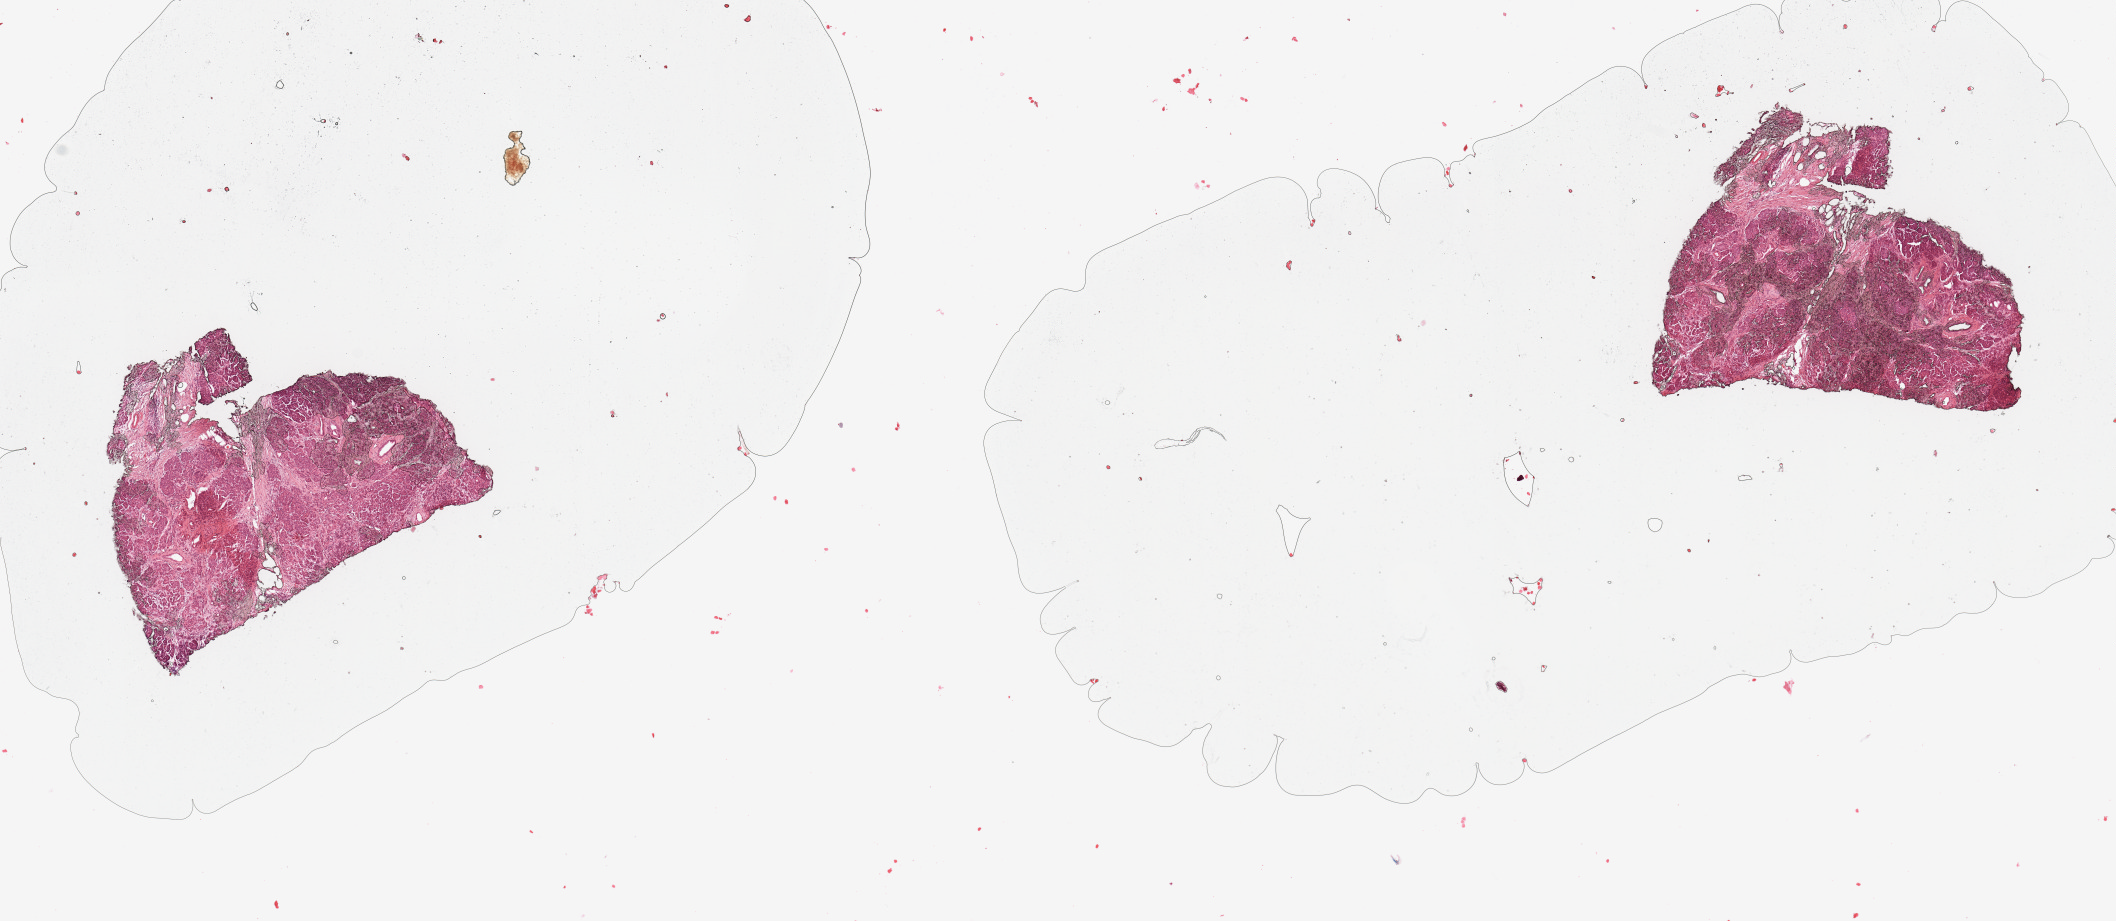
Hematoxylin and eosin (H&E) stained whole-slide image, low-resolution overview of the scanned area, about 16.7 x 7.3 mm. Normal (non-tumour) tissue sample, sampled site: pancreas. 60-year-old male patient.
• this section: normal (non-tumour) tissue from the same patient
• patient diagnosis: Infiltrating duct carcinoma, NOS